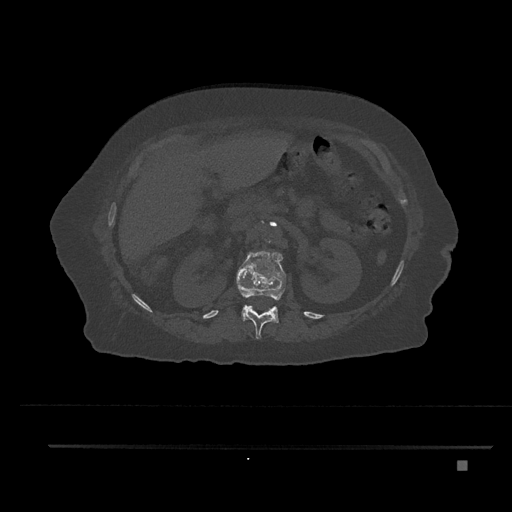
CT including the spine, one axial slice; slice 240 of 797 in the series (ordered by position); 120 kVp; bone window (W 1800 / L 400 HU); 0.5 mm slice thickness; 512 × 512 image matrix. Female patient, age 76 years. Case-level facts recorded for this patient, not image findings: primary cancer: lung; vertebrae with lytic lesions (as recorded): T11, L3.
Outlined on this slice (semi-automatic segmentation, software-assisted and operator-edited):
- L1 vertebra: bounding box <236,250,286,323> (left, top, right, bottom; pixels)
- T12 vertebra: <246,286,275,339>